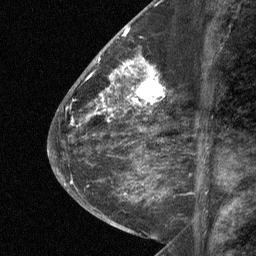
Breast MRI (dynamic contrast-enhanced), one sagittal slice; position 26 of 64 along the scan axis; dynamic contrast-enhanced study with each time point stored as its own series, time point 2 of 3 at this slice position (early post-contrast, ordered by acquisition time); 1.5 T; TE 4.8 ms, TR 27 ms; 2 mm slice thickness; 256 × 256 image matrix, field of view 180 × 180 mm. Female patient, age 59 years. Case-level facts recorded for this patient, not image findings: setting: breast cancer imaged before/during neoadjuvant chemotherapy; receptor status: triple-negative.
Structures marked on this image (semi-automatically segmented with operator editing):
- analysis volume of interest (the breast-tissue region the enhancement analysis was run in; not a lesion): bounding box <122,58,175,109> (left, top, right, bottom; pixels)
- tumour enhancement mask (voxels above the 90 % enhancement threshold inside the analysis volume of interest): <122,58,163,107>